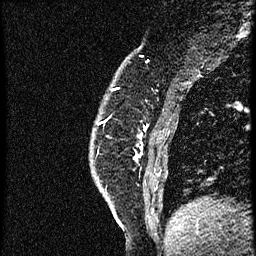
Breast MRI (dynamic contrast-enhanced), one sagittal slice. Slice 13 of 56 in the series (ordered by position). Dynamic contrast-enhanced study with each time point stored as its own series, time point 2 of 4 at this slice position (early post-contrast, ordered by acquisition time). 1.5 T. TE 4.2 ms, TR 18.9 ms. 2 mm slice thickness. 256 × 256 image matrix, field of view 200 × 200 mm. Female patient. Case-level facts recorded for this patient, not image findings: setting: breast cancer imaged before/during neoadjuvant chemotherapy; receptor status: HER2-positive.
Outlined on this slice (semi-automatically segmented with operator editing):
- analysis volume of interest (the breast-tissue region the enhancement analysis was run in; not a lesion): box from (x=136, y=101) to (x=170, y=189) px
- tumour enhancement mask (voxels above the 100 % enhancement threshold inside the analysis volume of interest): (x=136, y=128)–(x=147, y=158)